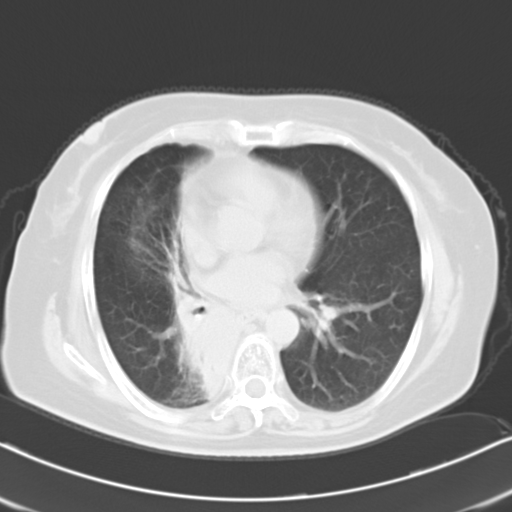
Chest CT, one axial slice; slice 10 of 21 in the series (ordered by position); lung window (W 1500 / L -600 HU); 10 mm slice thickness; 512 × 512 image matrix, field of view 326 × 326 mm. Female patient, age 61 years. From the clinical record (not read from this slice): clinical TNM (as recorded): T1b N0 M1b.
Outlined on this slice (bounding box drawn by a radiologist):
- lung tumour (recorded histology: squamous cell carcinoma): bounding box <164,268,250,415> (left, top, right, bottom; pixels)